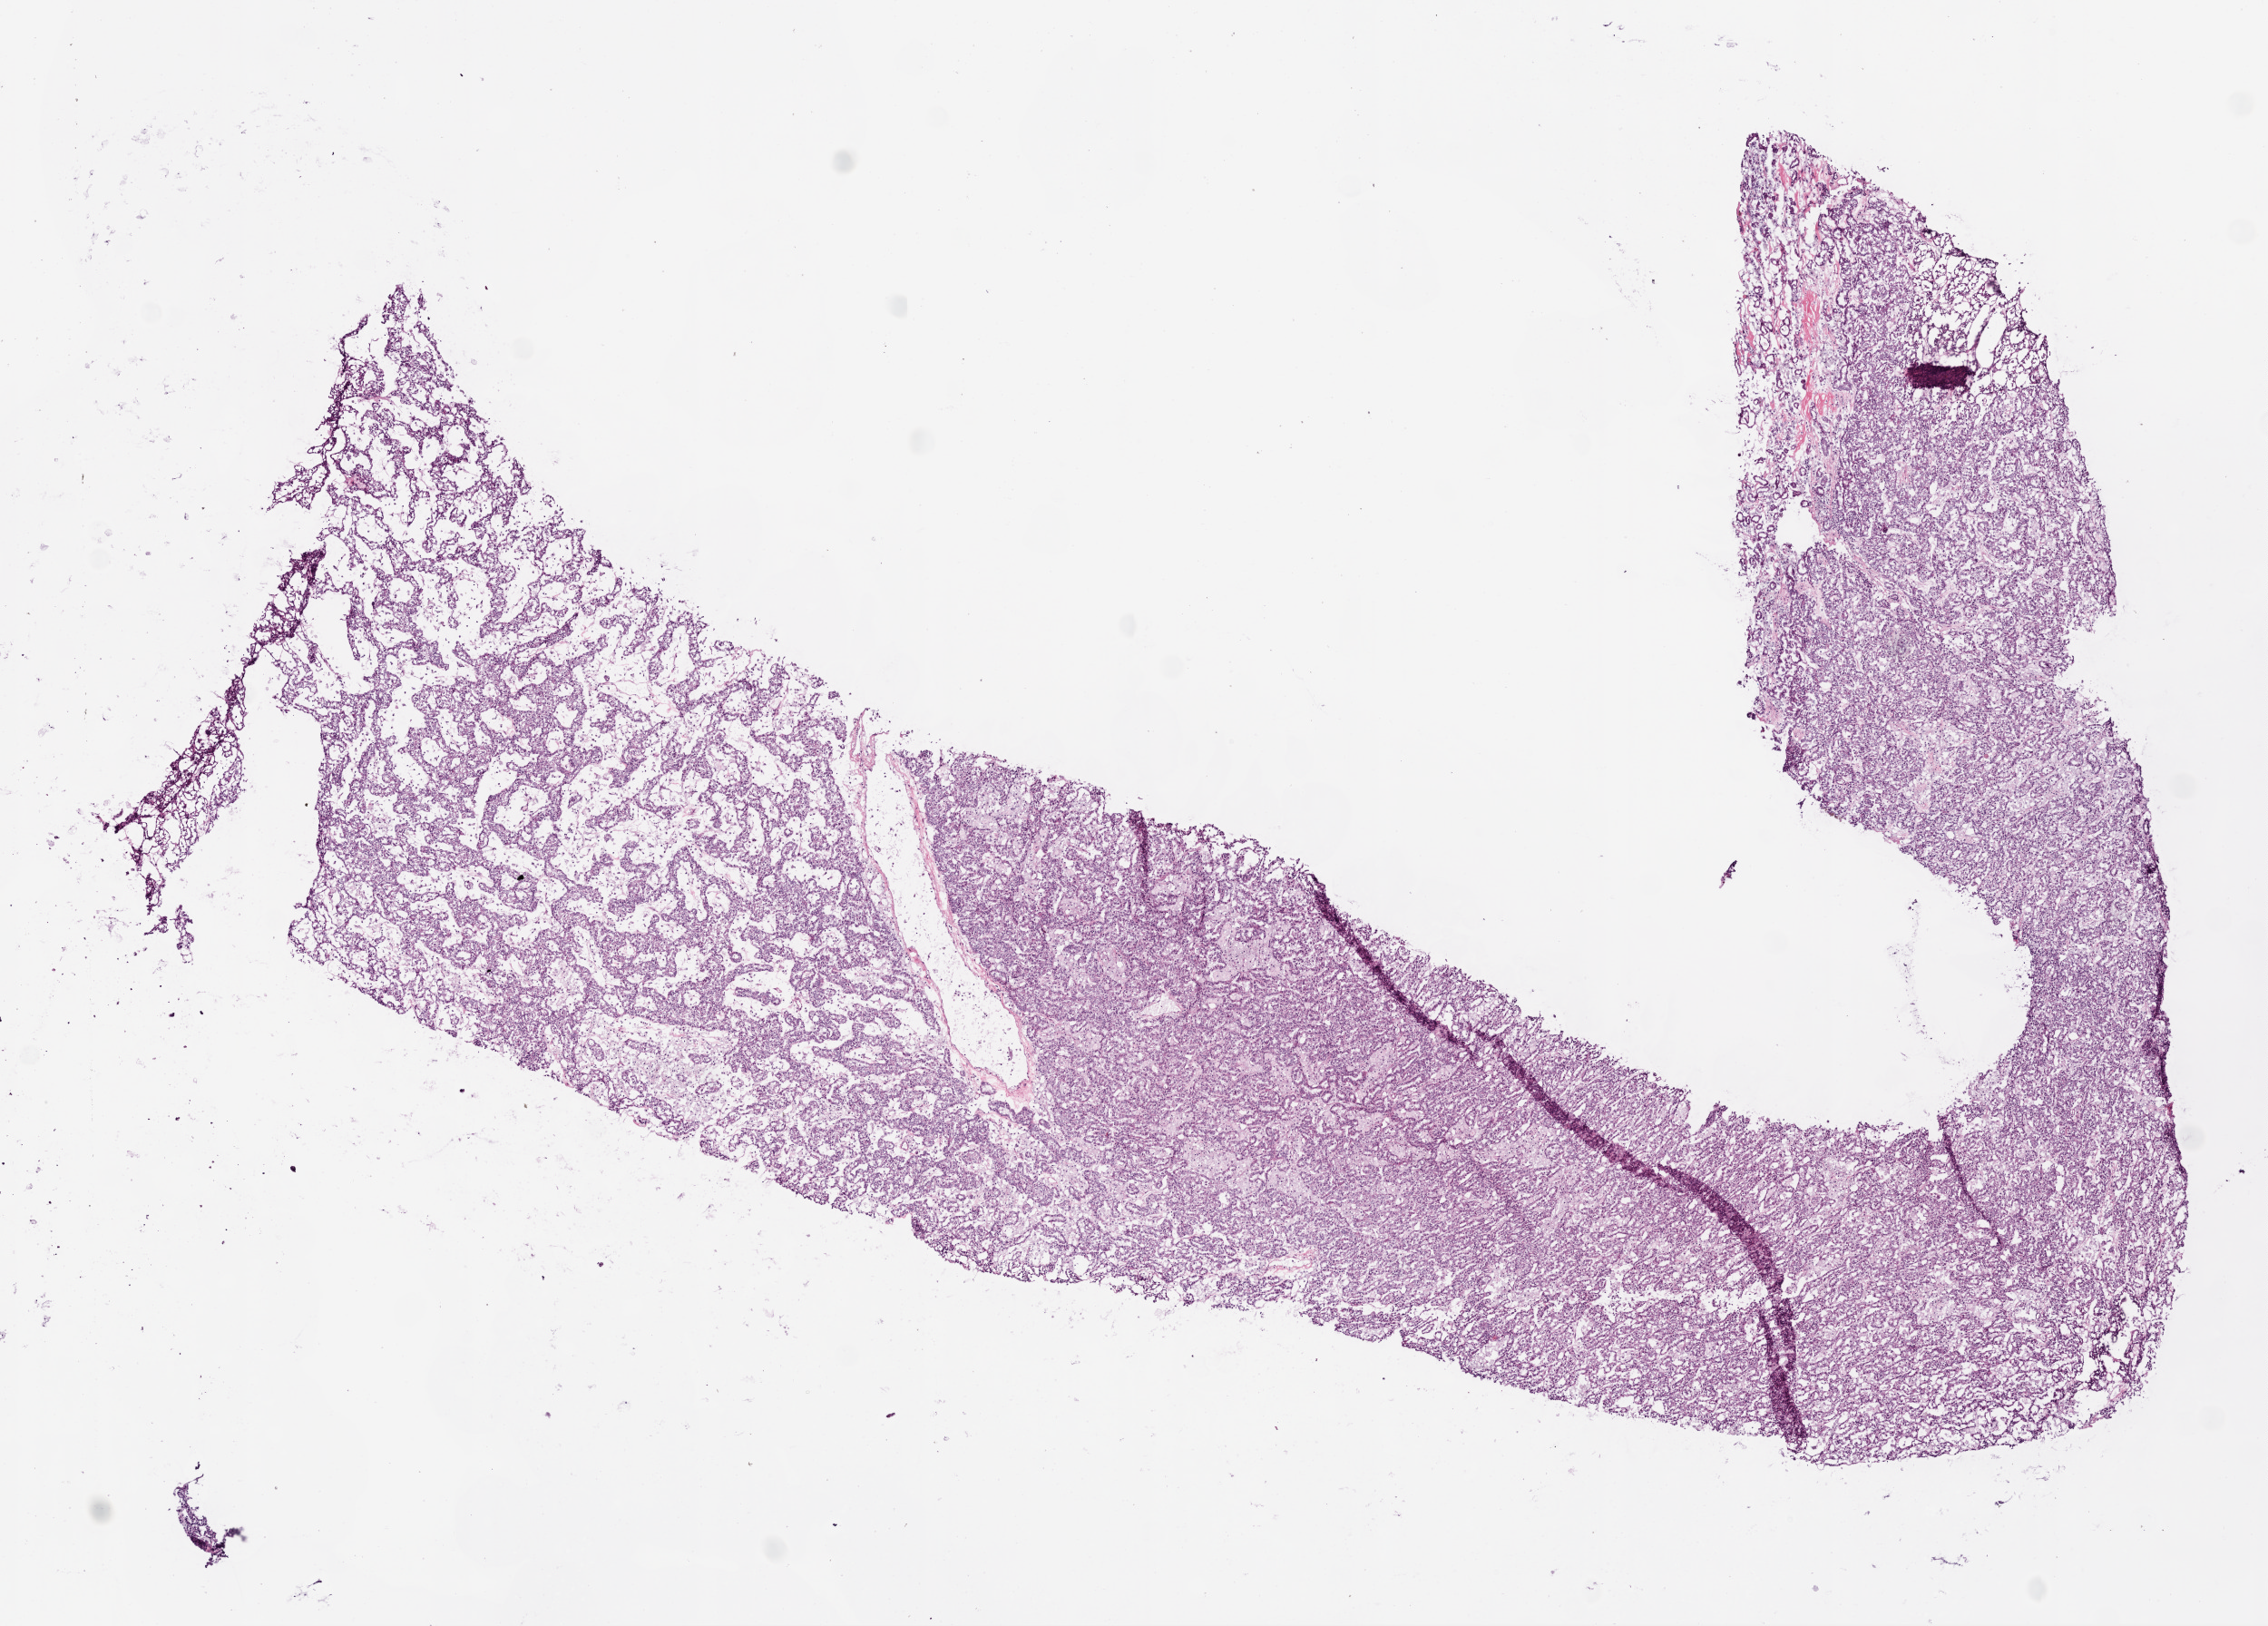
H&E whole-slide image, a low-resolution overview of the entire scanned area, about 10.0 x 7.2 mm (slide scanned at 20x); frozen section from the bottom of the tissue portion; sample: primary tumour, kidney. Male, age 64 years at initial diagnosis.
Histologic diagnosis: Papillary adenocarcinoma, NOS.